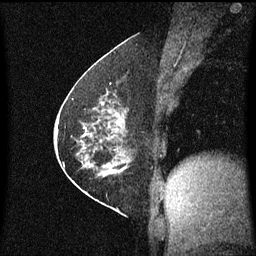
Breast MRI (dynamic contrast-enhanced), one sagittal slice. Slice 30 of 60 in the series (ordered by position). Dynamic contrast-enhanced series, image 2 of 3 at this slice position (ordered by acquisition). 1.5 T. TE 4.2 ms, TR 8.4 ms. 2 mm slice thickness. 256 × 256 image matrix. Patient: female, 60 years.
Outlined on this slice (semi-automatic segmentation, software-assisted and operator-edited):
- analysis volume of interest (the breast-tissue region the enhancement analysis was run in; not a lesion): bounding box (x1, y1, x2, y2) in pixels: (69, 66, 143, 193)
- tumour enhancement mask (voxels above the 70 % enhancement threshold inside the analysis volume of interest): (69, 68, 131, 171)